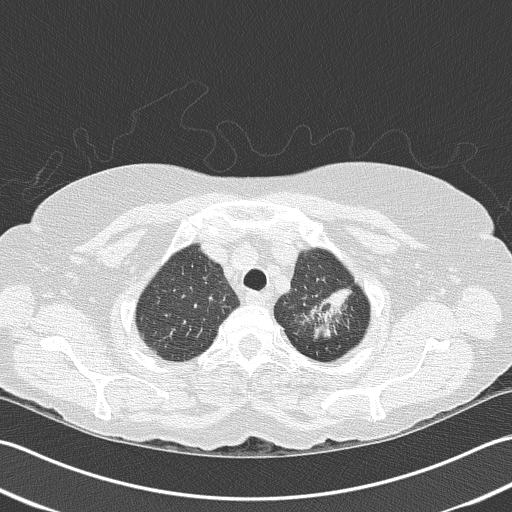
Axial slice from a low-dose chest CT screening exam; first (baseline) screen; lung window (W 1500 / L -600 HU); 2 mm slice thickness; lung (sharp) reconstruction kernel (B50f); slice 135 of 159 in the series. Female participant, aged 68 years at enrolment. Former smoker at enrolment.
Expert reader's lesion annotation, bounding box [x1, y1, x2, y2] px = [291, 265, 364, 335]. No non-calcified nodule or mass ≥4 mm was recorded by the screening reader at this exam.